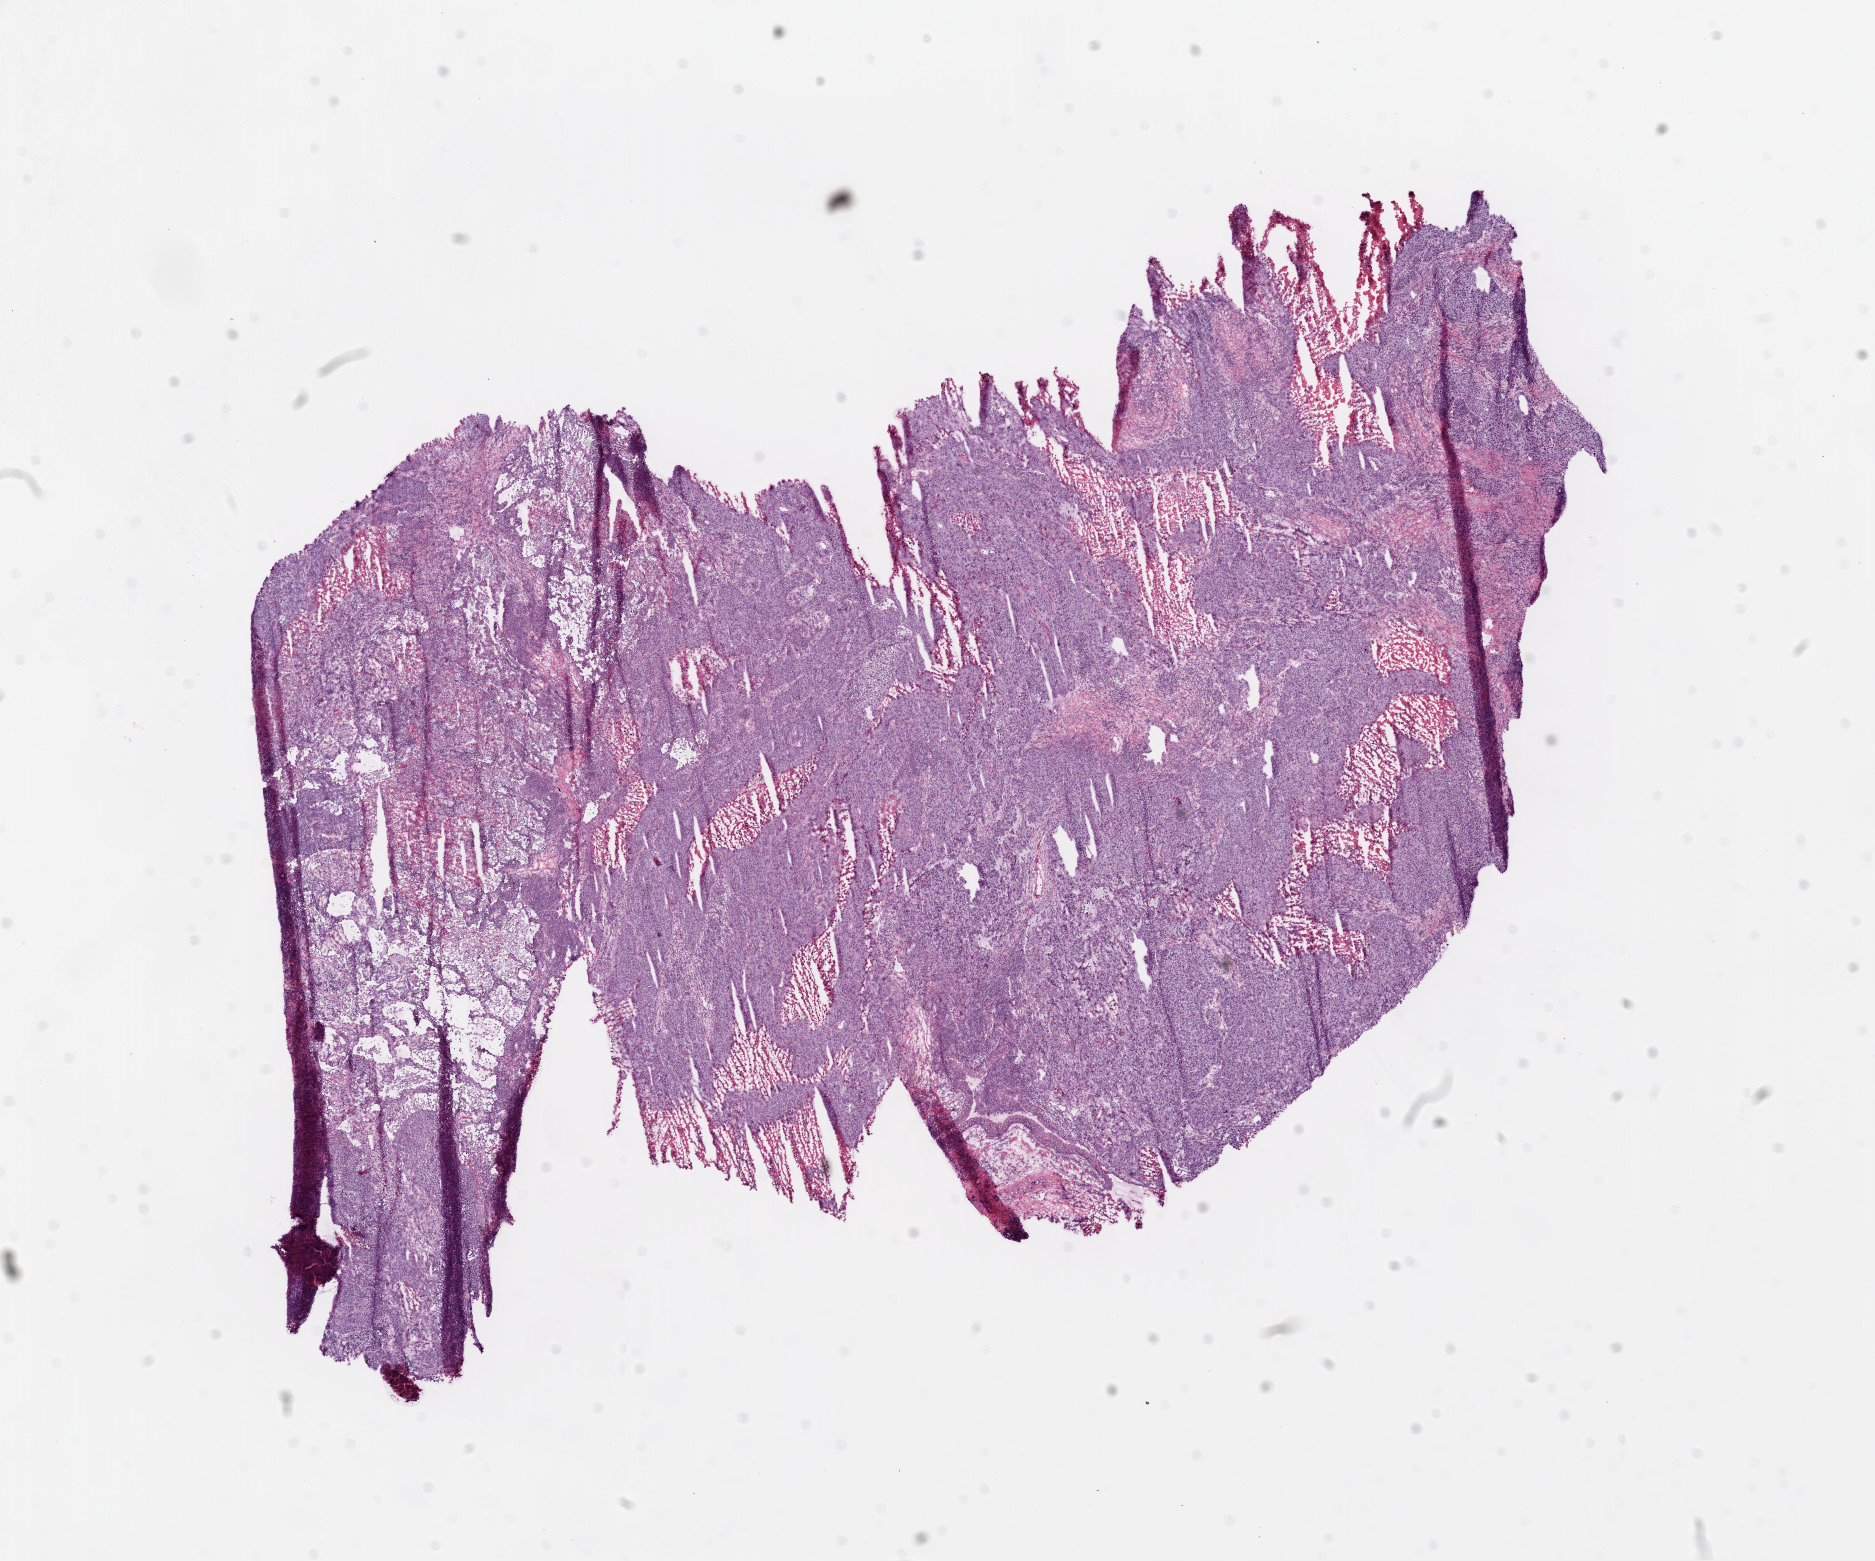
H&E-stained whole-slide image — shown as a low-resolution overview of the whole scanned area (about 15.0 x 12.5 mm); frozen section; primary tumour sample from the lung. Patient: male, age at initial diagnosis 71 years. Composition of this section per pathologist review: tumour cells 70%, tumour nuclei 80%, normal cells 5%, stromal cells 5%, necrosis 20%.
AJCC pathologic stage: IB. TNM: T2 N0 M0. Laterality: left. Diagnosis: Squamous cell carcinoma, NOS (upper lobe, lung).